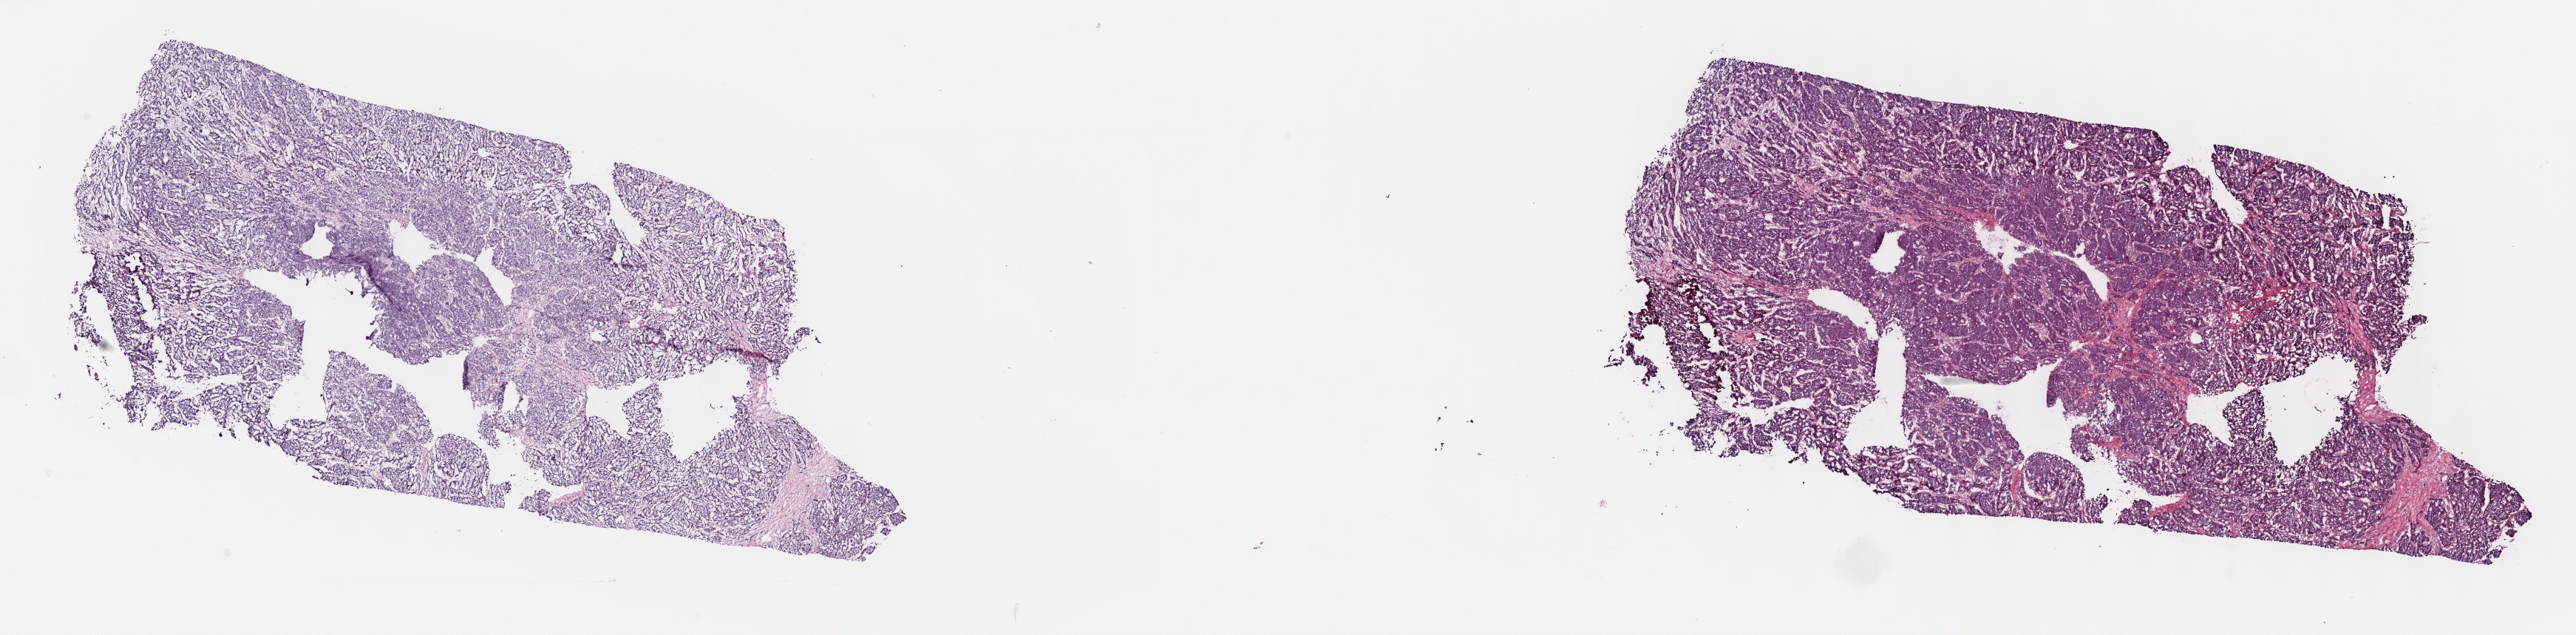
H&E whole-slide image — shown as a low-resolution overview of the whole scanned area (about 28.2 x 6.9 mm); frozen section from the top of the tissue portion; liver, primary tumour sample. Female patient; age at initial diagnosis 62 years. Histologic grade: G2 (moderately differentiated). Pathologist review of this section (percent, as recorded): tumour cells 90%, tumour nuclei 95%, normal cells 0%, stromal cells 10%, necrosis 0%. Infiltration values recorded for this section: lymphocyte infiltration 0%, monocyte infiltration 0%, neutrophil infiltration 0%.
- TNM: T2b N0 M0
- pathologic diagnosis: Combined hepatocellular carcinoma and cholangiocarcinoma
- AJCC pathologic stage: II (7th edition)